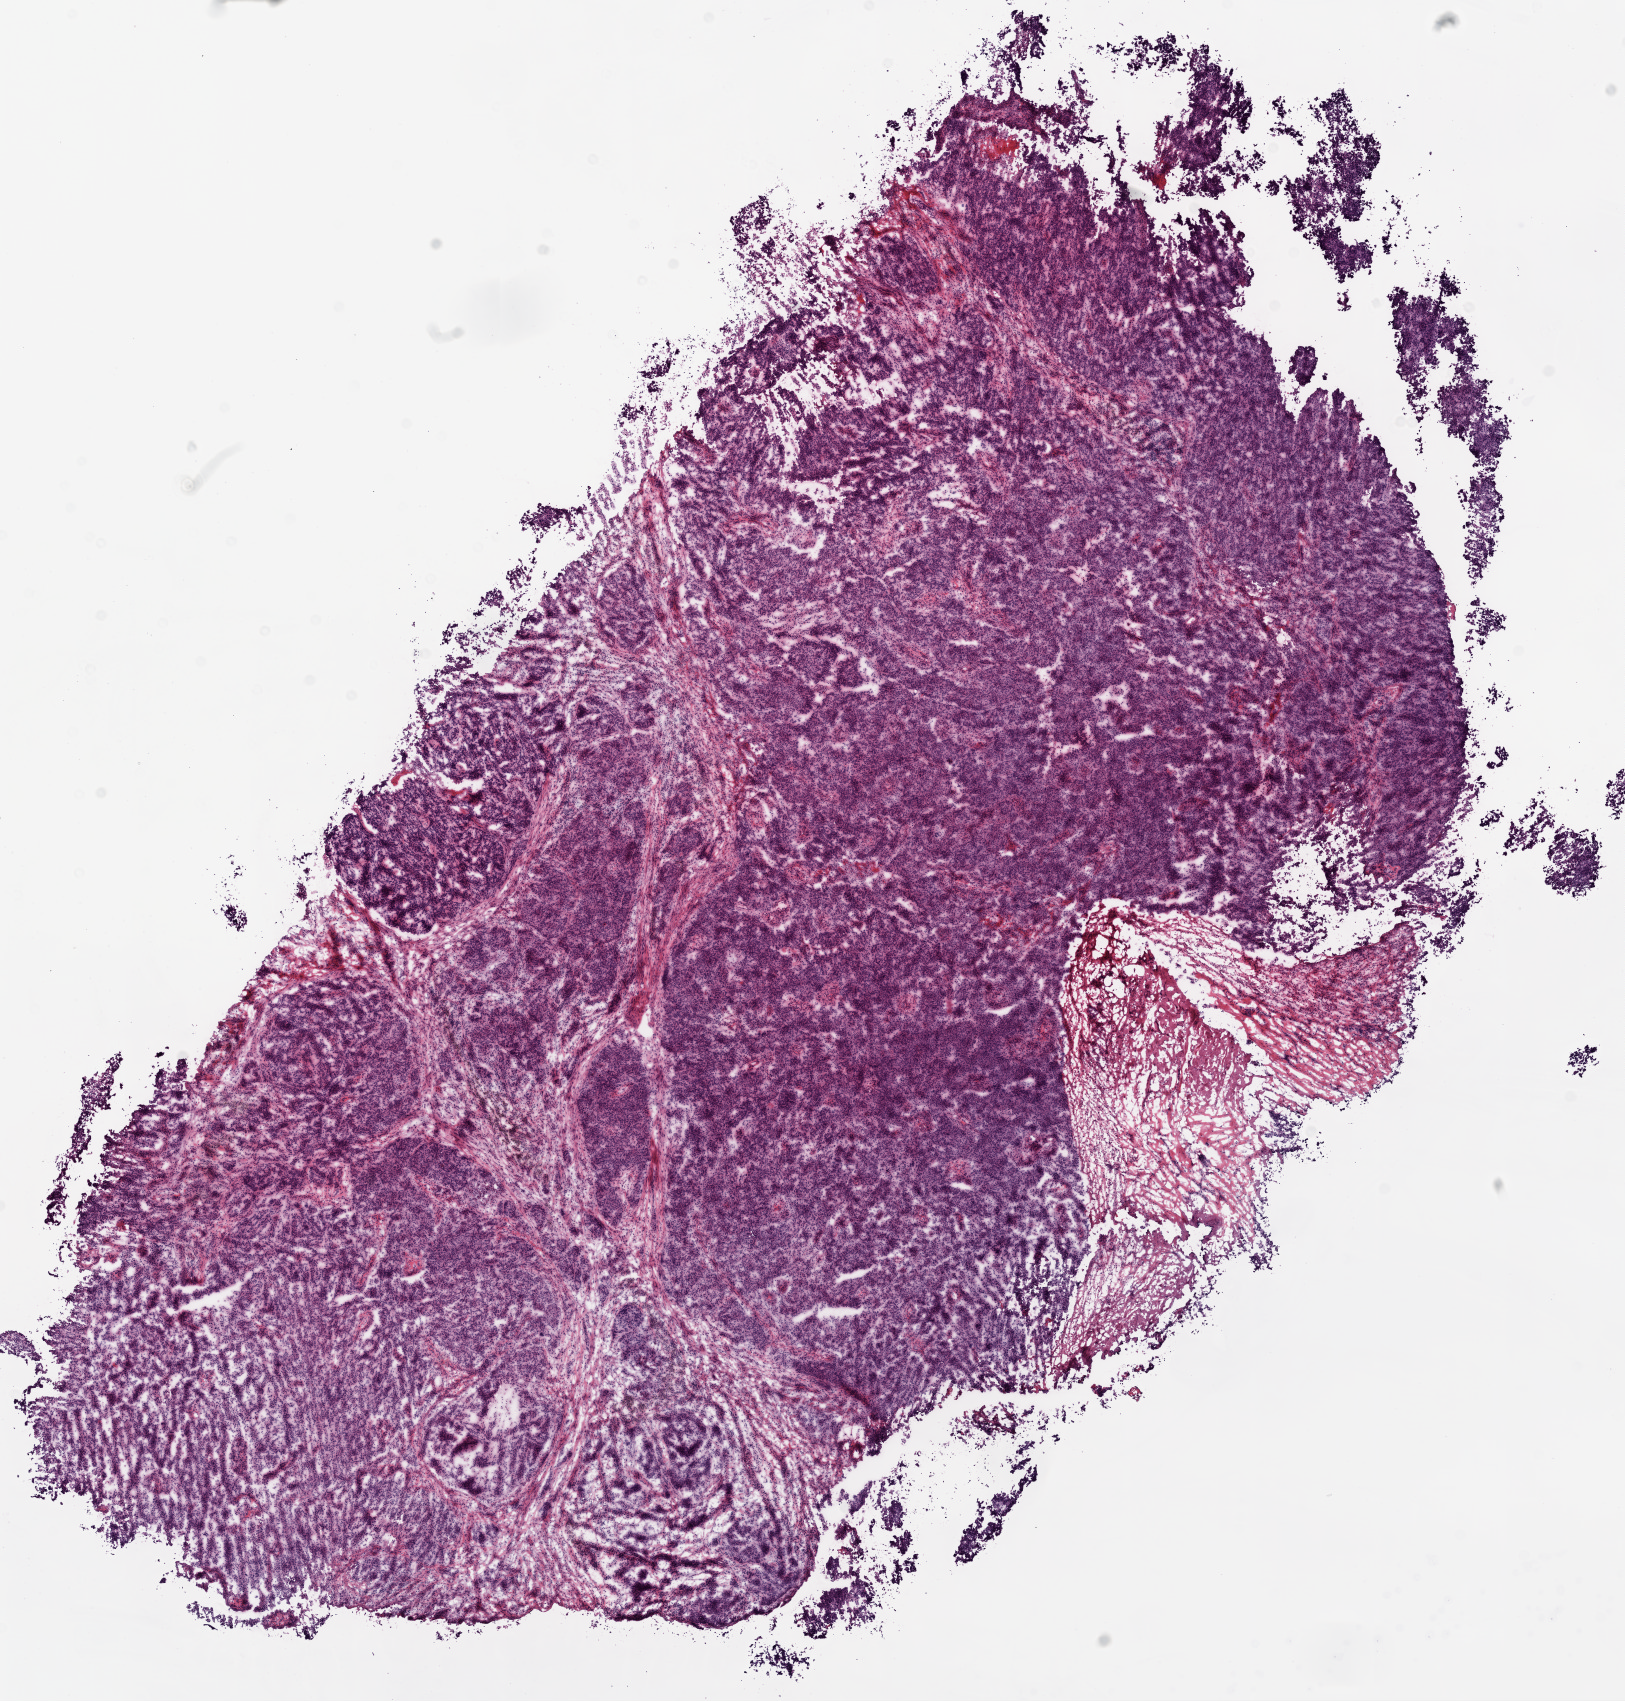
Whole-slide histology image, H&E-stained — shown as a low-resolution overview of the whole scanned area (about 13.0 x 13.6 mm); frozen section; primary tumour sample from the ovary. Female, age 73 years at initial diagnosis. Histologic grade: G3 (poorly differentiated). Slide review estimates, as recorded: tumour cells 80%, tumour nuclei 90%, normal cells 0%, stromal cells 10%, necrosis 10%.
* FIGO stage: IIIC
* pathologic diagnosis: Serous cystadenocarcinoma, NOS